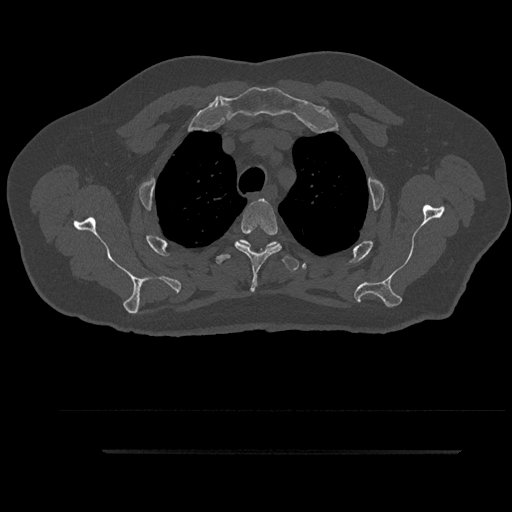
CT including the spine, one axial slice; position 708 of 797 along the scan axis; reconstruction kernel Br40s/3; 120 kVp; bone window (W 1800 / L 400 HU); 0.5 mm slice thickness; 512 × 512 image matrix, field of view 432 × 432 mm. Male patient, age 63 years. From the clinical record (not read from this slice): primary cancer: renal; vertebrae with lytic lesions (as recorded): T8.
Structures marked on this image (semi-automatic segmentation, software-assisted and operator-edited):
- T3 vertebra: bounding box <235,198,281,292> (left, top, right, bottom; pixels)
- T4 vertebra: <215,240,299,271>